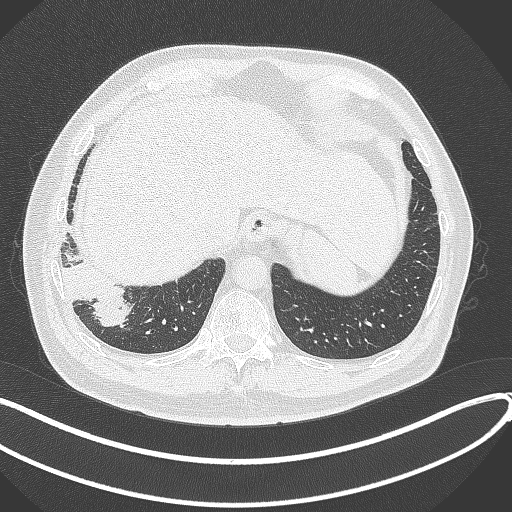
Chest CT, one axial slice; position 60 of 360 along the scan axis; reconstruction kernel B70f; 120 kVp; lung window (W 1500 / L -600 HU); 512 × 512 image matrix. Male patient, age 59 years.
Structures marked on this image (bounding box drawn by a radiologist):
- lung tumour (recorded histology: adenocarcinoma): bounding box (x1, y1, x2, y2) in pixels: (58, 256, 133, 331)